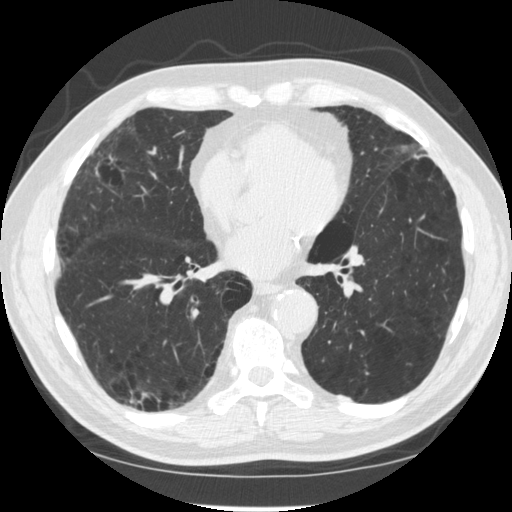
Axial slice from a low-dose chest CT screening exam; second screening round (one year after baseline); lung window (W 1500 / L -600 HU); standard (soft-tissue) reconstruction kernel (STANDARD); 120 kVp; 512 × 512 image matrix. Male participant, aged 70 years at enrolment. Former smoker at enrolment.
- Expert reader's lesion annotation, box from (x=118, y=374) to (x=170, y=434) px.
- The screening reader recorded 2 non-calcified nodules or masses ≥4 mm on this exam (right lower lobe, right lower lobe); which of them this box marks is not recorded.
- Official screen result: negative screen, significant abnormalities not suspicious for lung cancer.
- Participant outcome: lung cancer diagnosed 617 days after this screen — squamous cell carcinoma, NOS, right upper lobe, poorly differentiated (G3), stage IV (AJCC 6th edition).